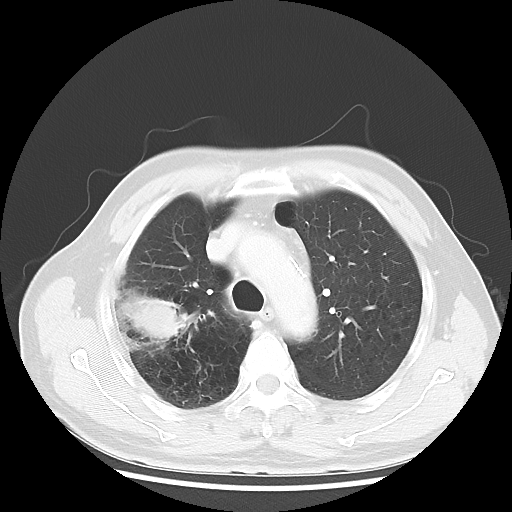
Chest CT, one axial slice; slice 37 of 50 in the series (ordered by position); 120 kVp; lung window (W 1500 / L -600 HU); 5 mm slice thickness; 512 × 512 image matrix, field of view 360 × 360 mm. Male patient, age 69 years. From the clinical record (not read from this slice): clinical TNM (as recorded): T3 N0 M0; histopathological grade: G3.
Annotated regions visible in this slice (bounding box drawn by a radiologist):
- lung tumour (recorded histology: adenocarcinoma): bounding box [x1, y1, x2, y2] px = [117, 288, 197, 354]